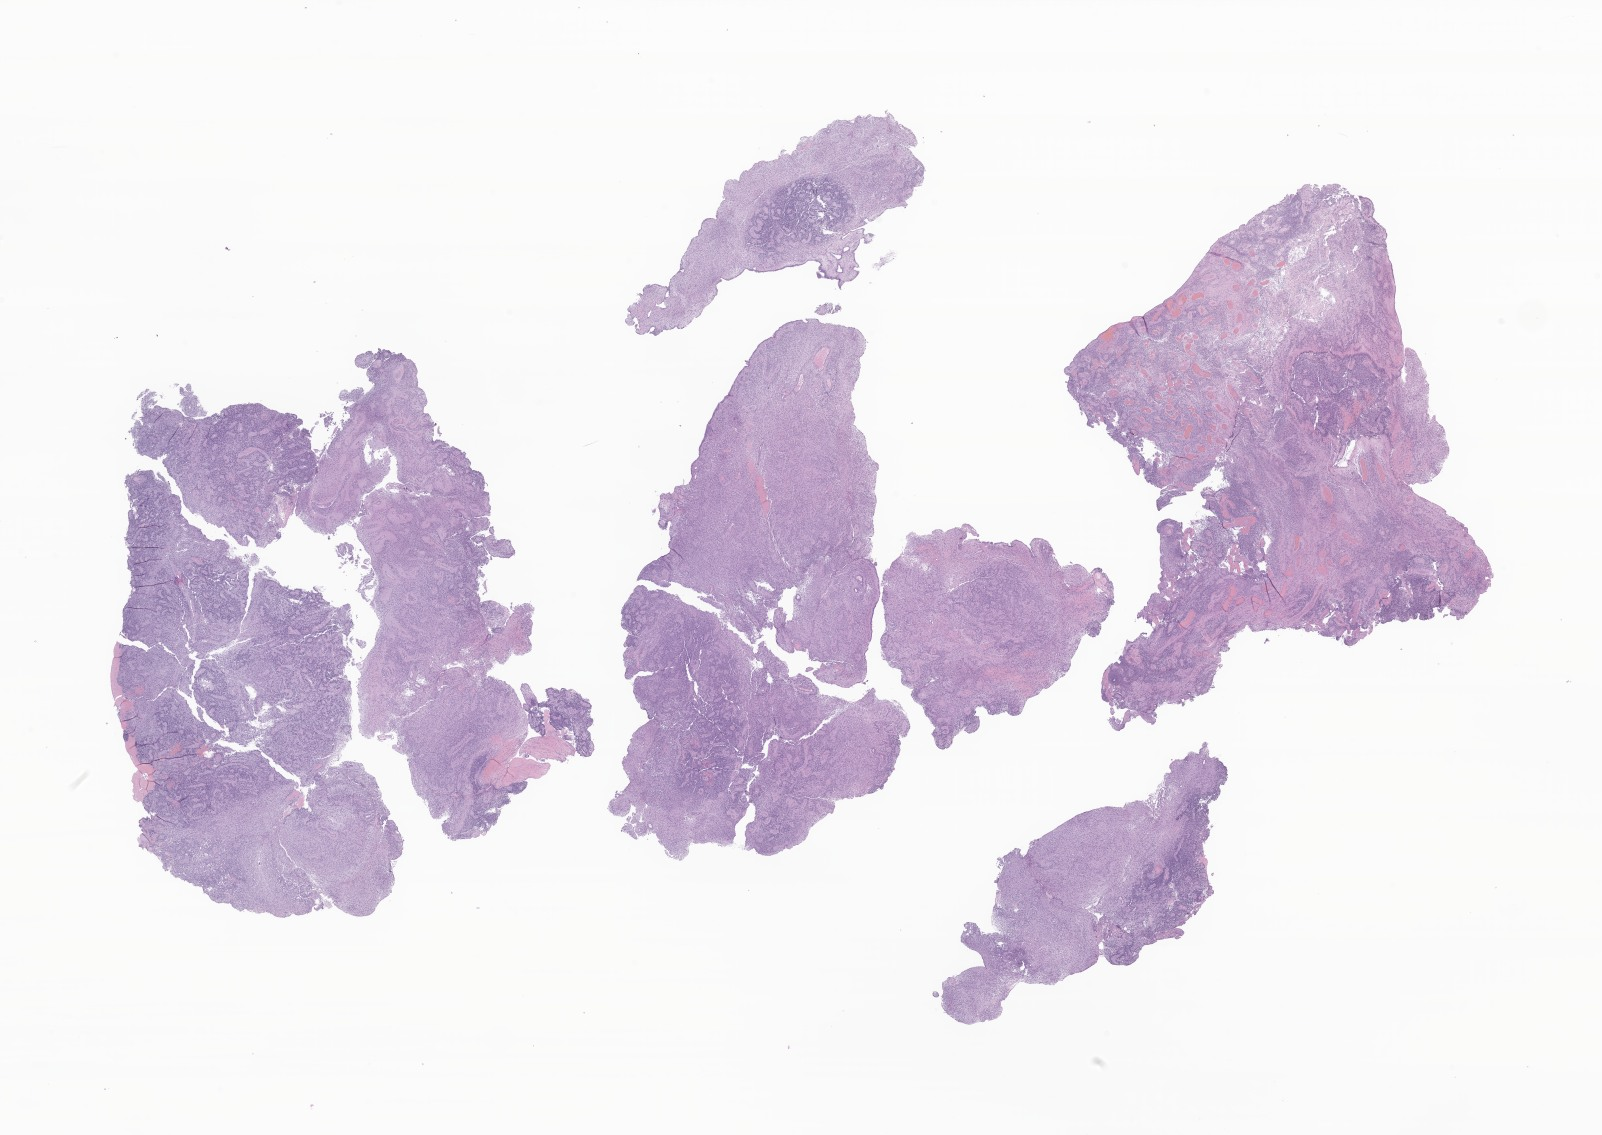
Digitized haematoxylin and eosin-stained section of tumor tissue from the brain, a low-resolution overview of the entire scanned area, about 27.0 x 19.1 mm. Formalin-fixed paraffin-embedded section. Male patient, age 493 days.
Recorded diagnosis: Ependymoma, NOS.